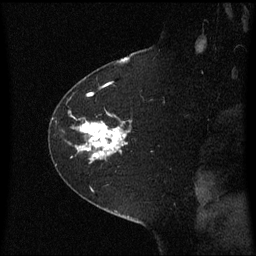
Breast MRI (dynamic contrast-enhanced), one sagittal slice; slice 47 of 60 in the series (ordered by position); dynamic contrast-enhanced series, image 2 of 3 at this slice position (ordered by acquisition); 1.5 T; TE 4.2 ms, TR 8.4 ms; 256 × 256 image matrix. Patient: female, 60 years. From the clinical record (not read from this slice): setting: breast cancer imaged before/during neoadjuvant chemotherapy; receptor status: triple-negative.
Structures marked on this image (semi-automatically segmented with operator editing):
- analysis volume of interest (the breast-tissue region the enhancement analysis was run in; not a lesion): bounding box [x1, y1, x2, y2] px = [50, 99, 133, 180]
- tumour enhancement mask (voxels above the 70 % enhancement threshold inside the analysis volume of interest): [78, 122, 127, 158]